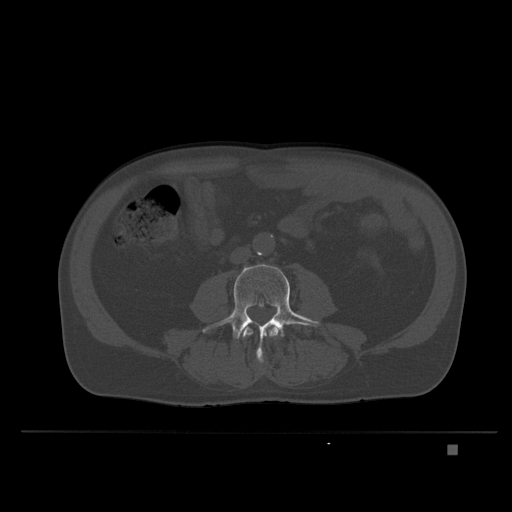
CT including the spine, one axial slice; position 80 of 435 along the scan axis; bone window (W 1800 / L 400 HU); 1.5 mm slice thickness; 512 × 512 image matrix, field of view 434 × 434 mm. Male patient, age 73 years. From the clinical record (not read from this slice): primary cancer: skin.
Annotated regions visible in this slice (semi-automatically segmented with operator editing):
- L3 vertebra: bounding box [x1, y1, x2, y2] px = [242, 325, 278, 339]
- L4 vertebra: [202, 264, 321, 363]